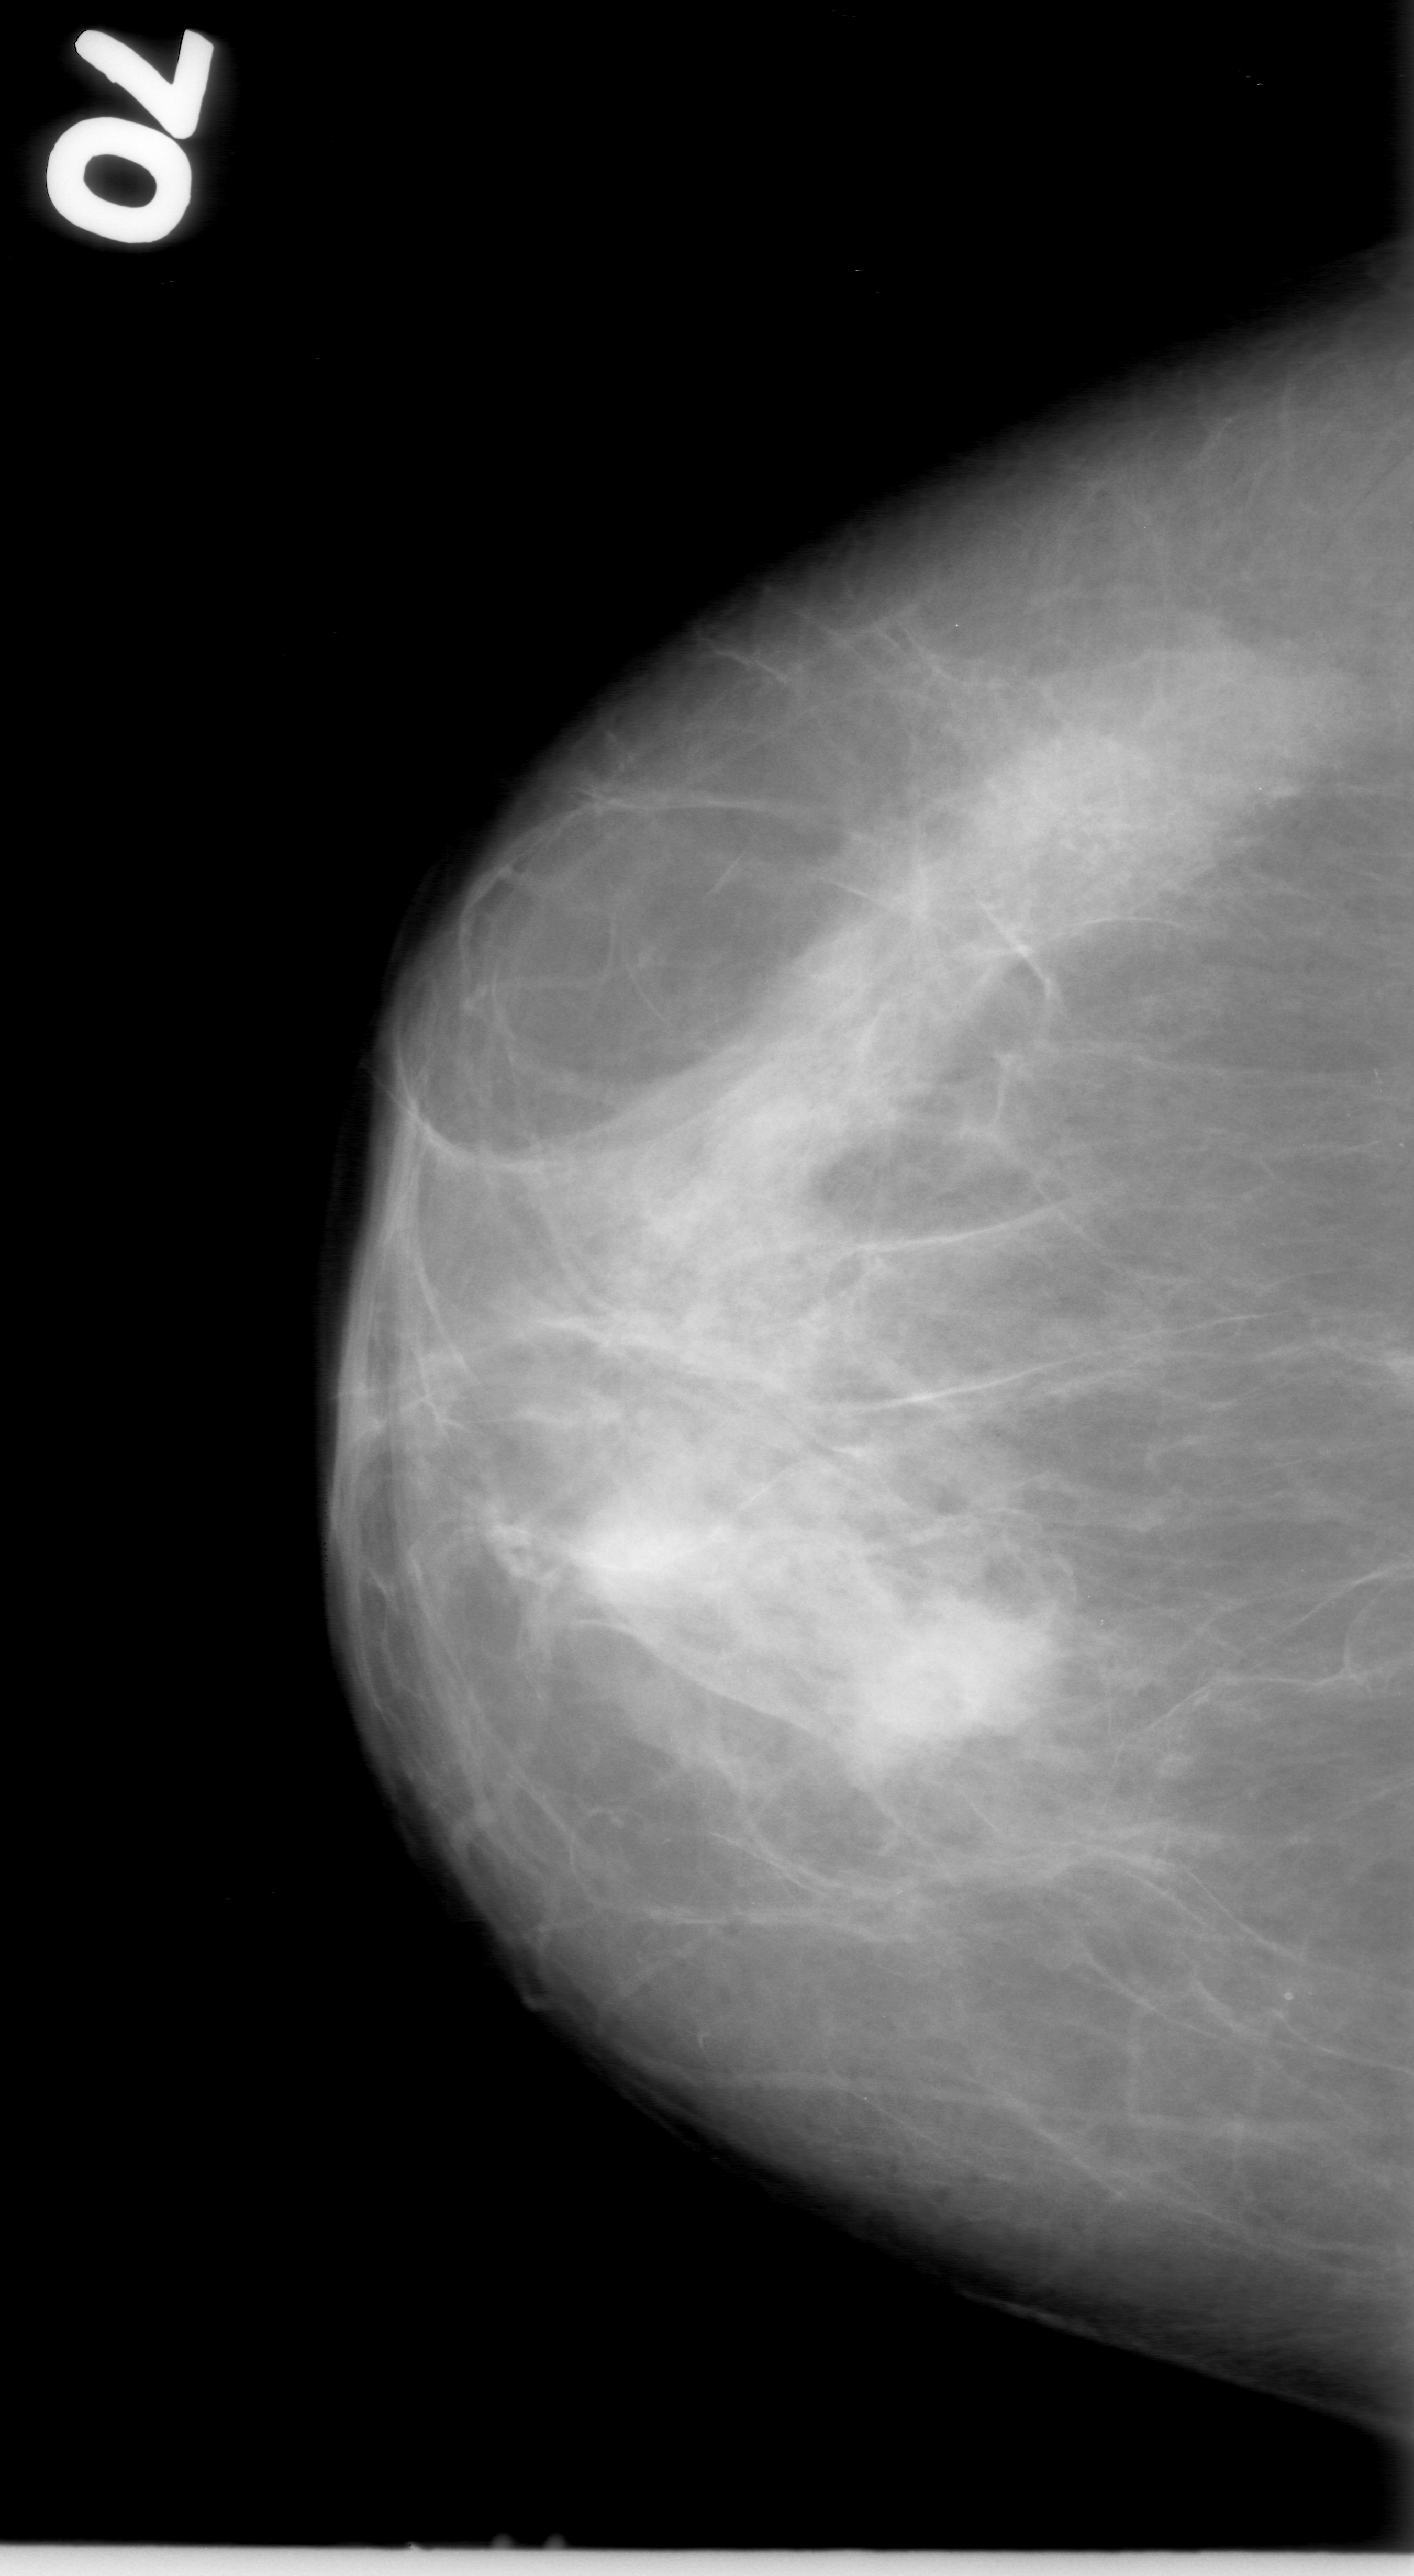
Digitized screen-film mammogram; right breast; CC view; BI-RADS breast density category 2 (scale 1–4).
Marked findings (only marked abnormalities are described; nothing is implied about the rest of the image): mass, shape irregular, margins ill defined; BI-RADS assessment category 3; subtlety rating 4 on a 1 (subtle) to 5 (obvious) scale; pathology (as recorded): malignant.